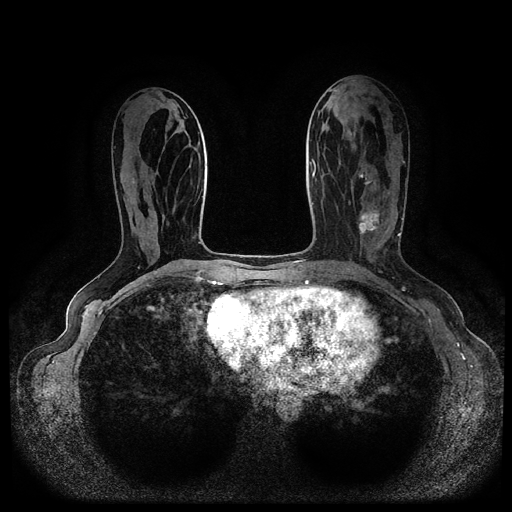
Breast MRI (dynamic contrast-enhanced, multi-phase), one axial slice. Slice 44 of 116 in the series (ordered by position). Dynamic contrast-enhanced series, time point 2 of 5 at this slice position (early post-contrast). 1.5 T. TE 2.6 ms, TR 5.3 ms. 2 mm slice thickness. 512 × 512 image matrix, field of view 350 × 350 mm. Female patient, age 45 years.
Structures marked on this image (semi-automatic segmentation, software-assisted and operator-edited):
- breast lesion (labelled 'tumour' in the annotation; benign lesions carry a separate 'benign' label): bounding box [x1, y1, x2, y2] px = [356, 199, 386, 239]